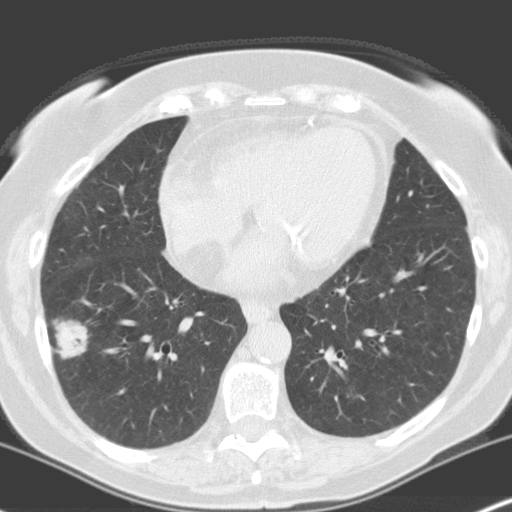
Low-dose screening chest CT, one axial slice; position 70 of 160 along the scan axis; lung window (W 1500 / L -600 HU); 3.2 mm slice thickness; 512 × 512 image matrix, field of view 316 × 316 mm.
Structures marked on this image (outlined manually by an expert reader):
- lesion 1 (tumor, lower lobe of right lung): bounding box [x1, y1, x2, y2] px = [55, 320, 89, 359]